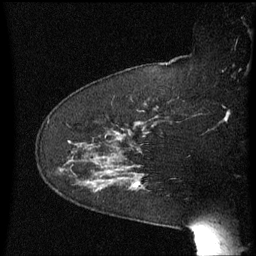
Breast MRI (dynamic contrast-enhanced), one sagittal slice; slice 45 of 60 in the series (ordered by position); dynamic contrast-enhanced series, image 2 of 3 at this slice position (ordered by acquisition); 1.5 T; TE 4.2 ms, TR 8.4 ms; 256 × 256 image matrix, field of view 200 × 200 mm. Patient: female, 64 years. From the clinical record (not read from this slice): setting: breast cancer imaged before/during neoadjuvant chemotherapy; receptor status: HER2-positive.
Annotated regions visible in this slice (semi-automatic segmentation, software-assisted and operator-edited):
- analysis volume of interest (the breast-tissue region the enhancement analysis was run in; not a lesion): bounding box (x1, y1, x2, y2) in pixels: (68, 158, 148, 211)
- tumour enhancement mask (voxels above the 70 % enhancement threshold inside the analysis volume of interest): (135, 184, 137, 187)